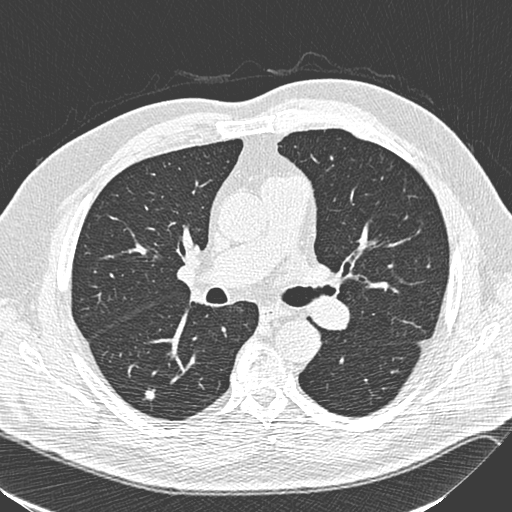
Low-dose screening chest CT, one axial slice; position 152 of 248 along the scan axis; 120 kVp; lung window (W 1500 / L -600 HU); 1.3 mm slice thickness; 512 × 512 image matrix, field of view 357 × 357 mm.
Annotated regions visible in this slice (expert manual segmentation):
- lesion 1 (tumor, lower lobe of right lung): bounding box [x1, y1, x2, y2] px = [145, 390, 156, 401]